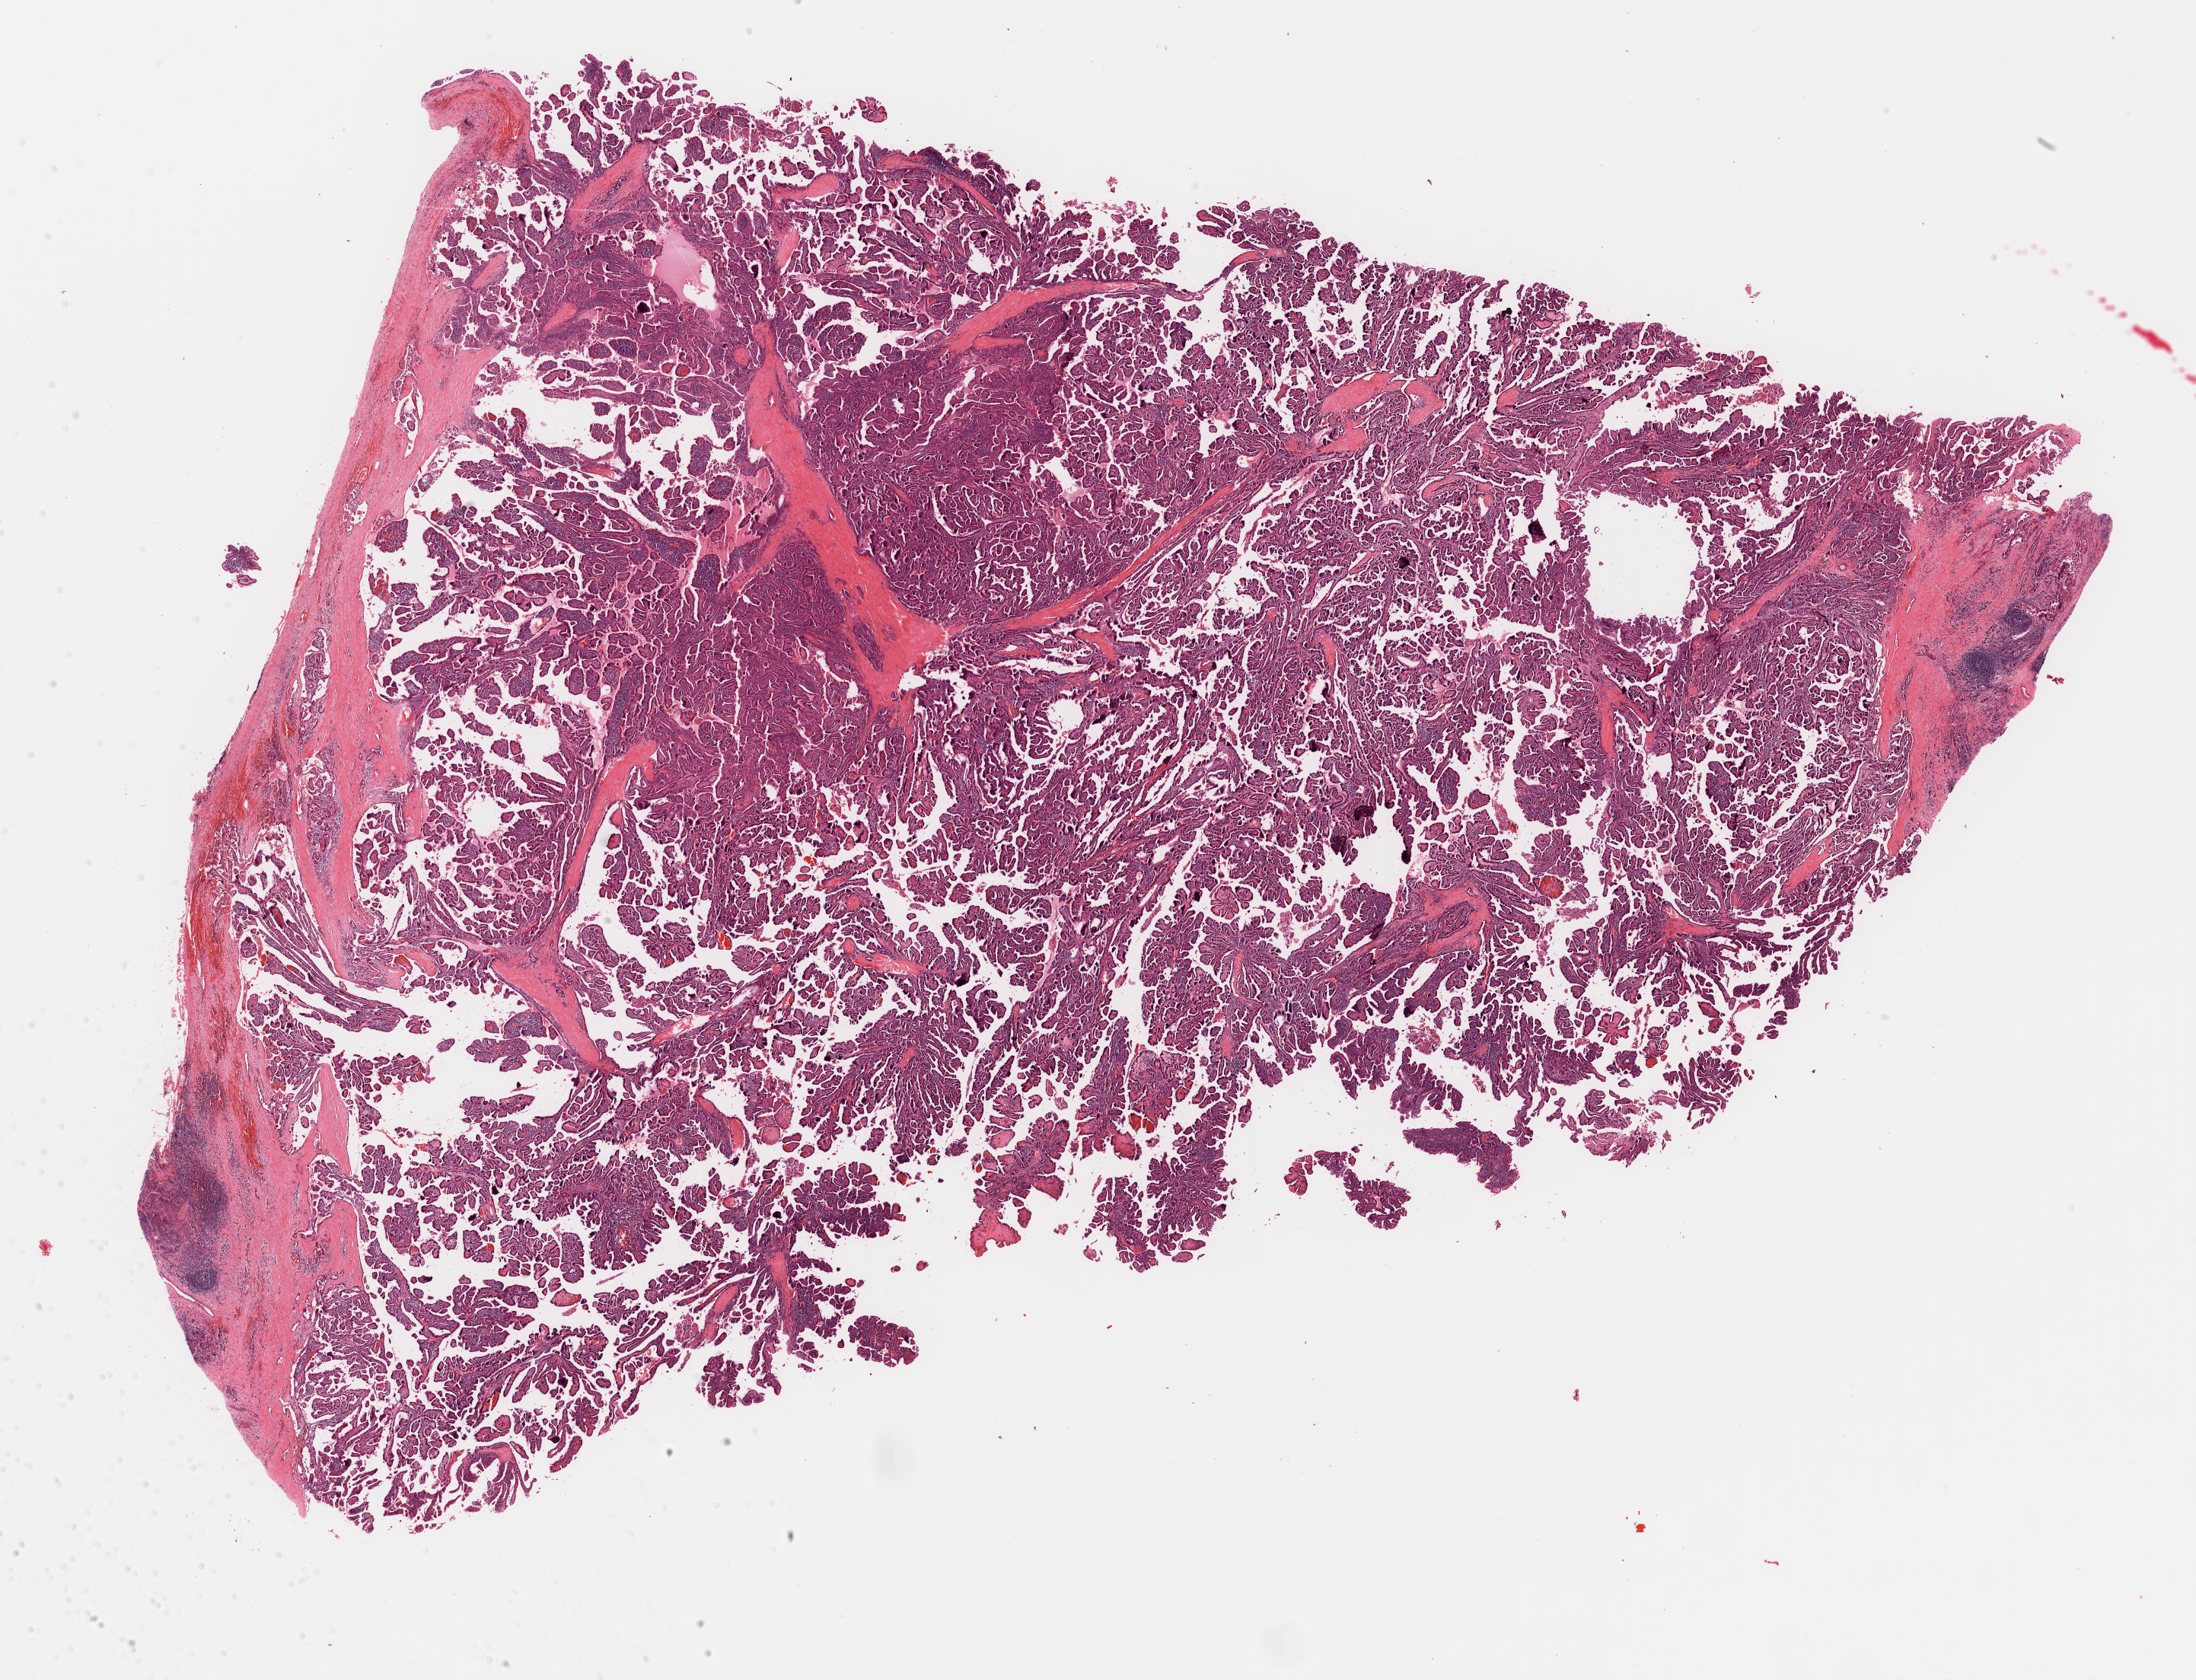
Digitized H&E-stained tissue section (whole slide), low-resolution overview of the scanned area, about 22.8 x 17.4 mm (from a 40x scan); formalin-fixed paraffin-embedded (FFPE) diagnostic section; sample: primary tumour, thyroid. Female patient; age at initial diagnosis 30 years.
AJCC pathologic stage: I (7th edition). Histologic diagnosis: Papillary adenocarcinoma, NOS (thyroid gland).